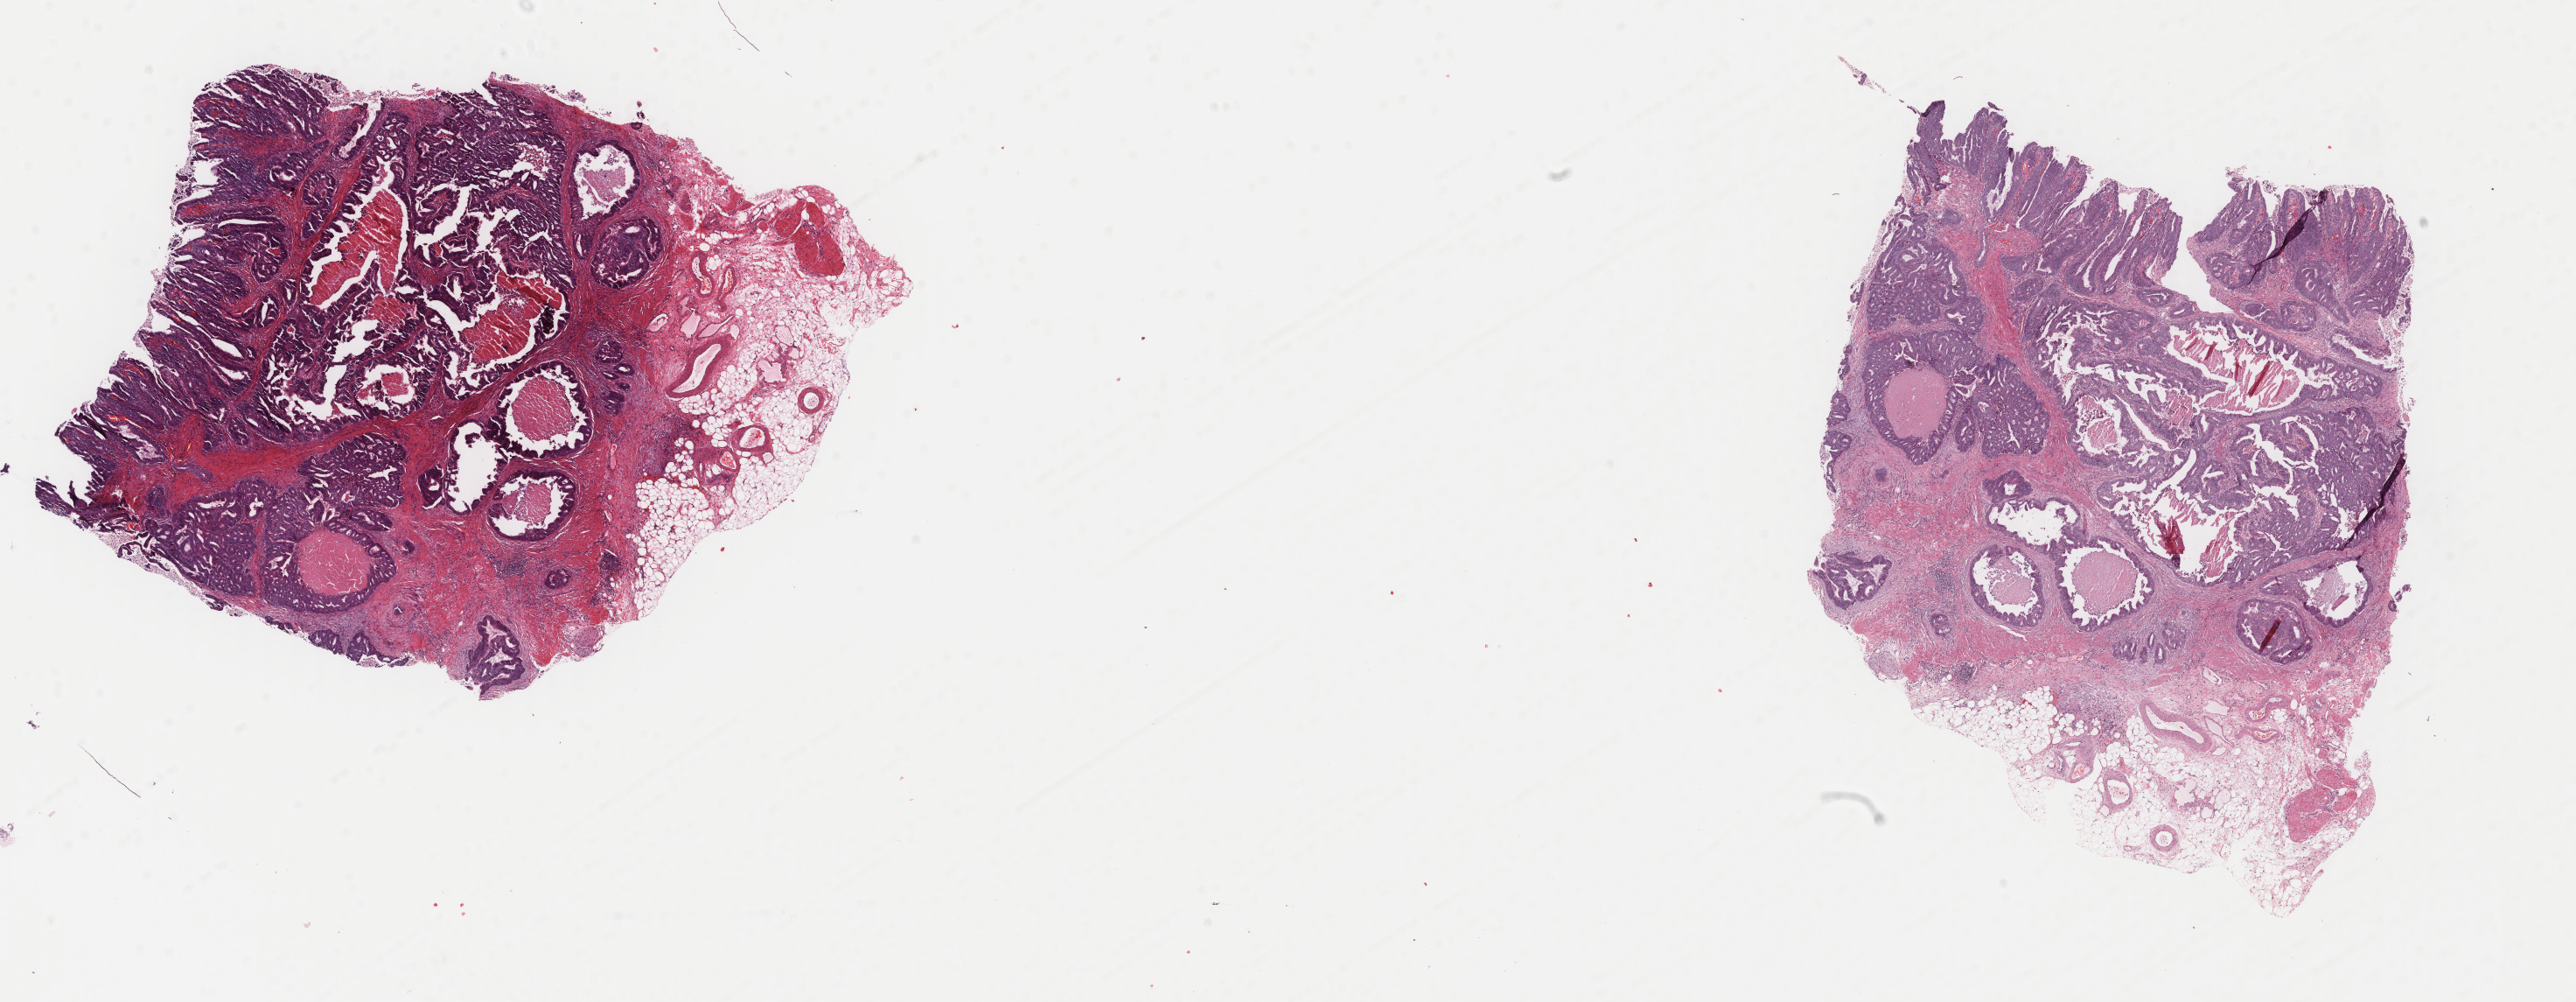
Whole-slide histology image, H&E — shown as a low-resolution overview of the whole scanned area (about 23.4 x 9.1 mm, acquisition: 40x scan). Frozen section. Primary tumour sample from the colon. Female, age 68 years at initial diagnosis. Slide review estimates, as recorded: tumour cells 60%, tumour nuclei 80%, normal cells 0%, stromal cells 30%, necrosis 10%. Infiltration values recorded for this section: lymphocyte infiltration 0%, monocyte infiltration 0%, neutrophil infiltration 0%.
Histologic diagnosis: Adenocarcinoma, NOS (ascending colon). Lymph nodes positive (case pathology): 5 of 30 examined. AJCC pathologic stage: IIIC (6th edition).